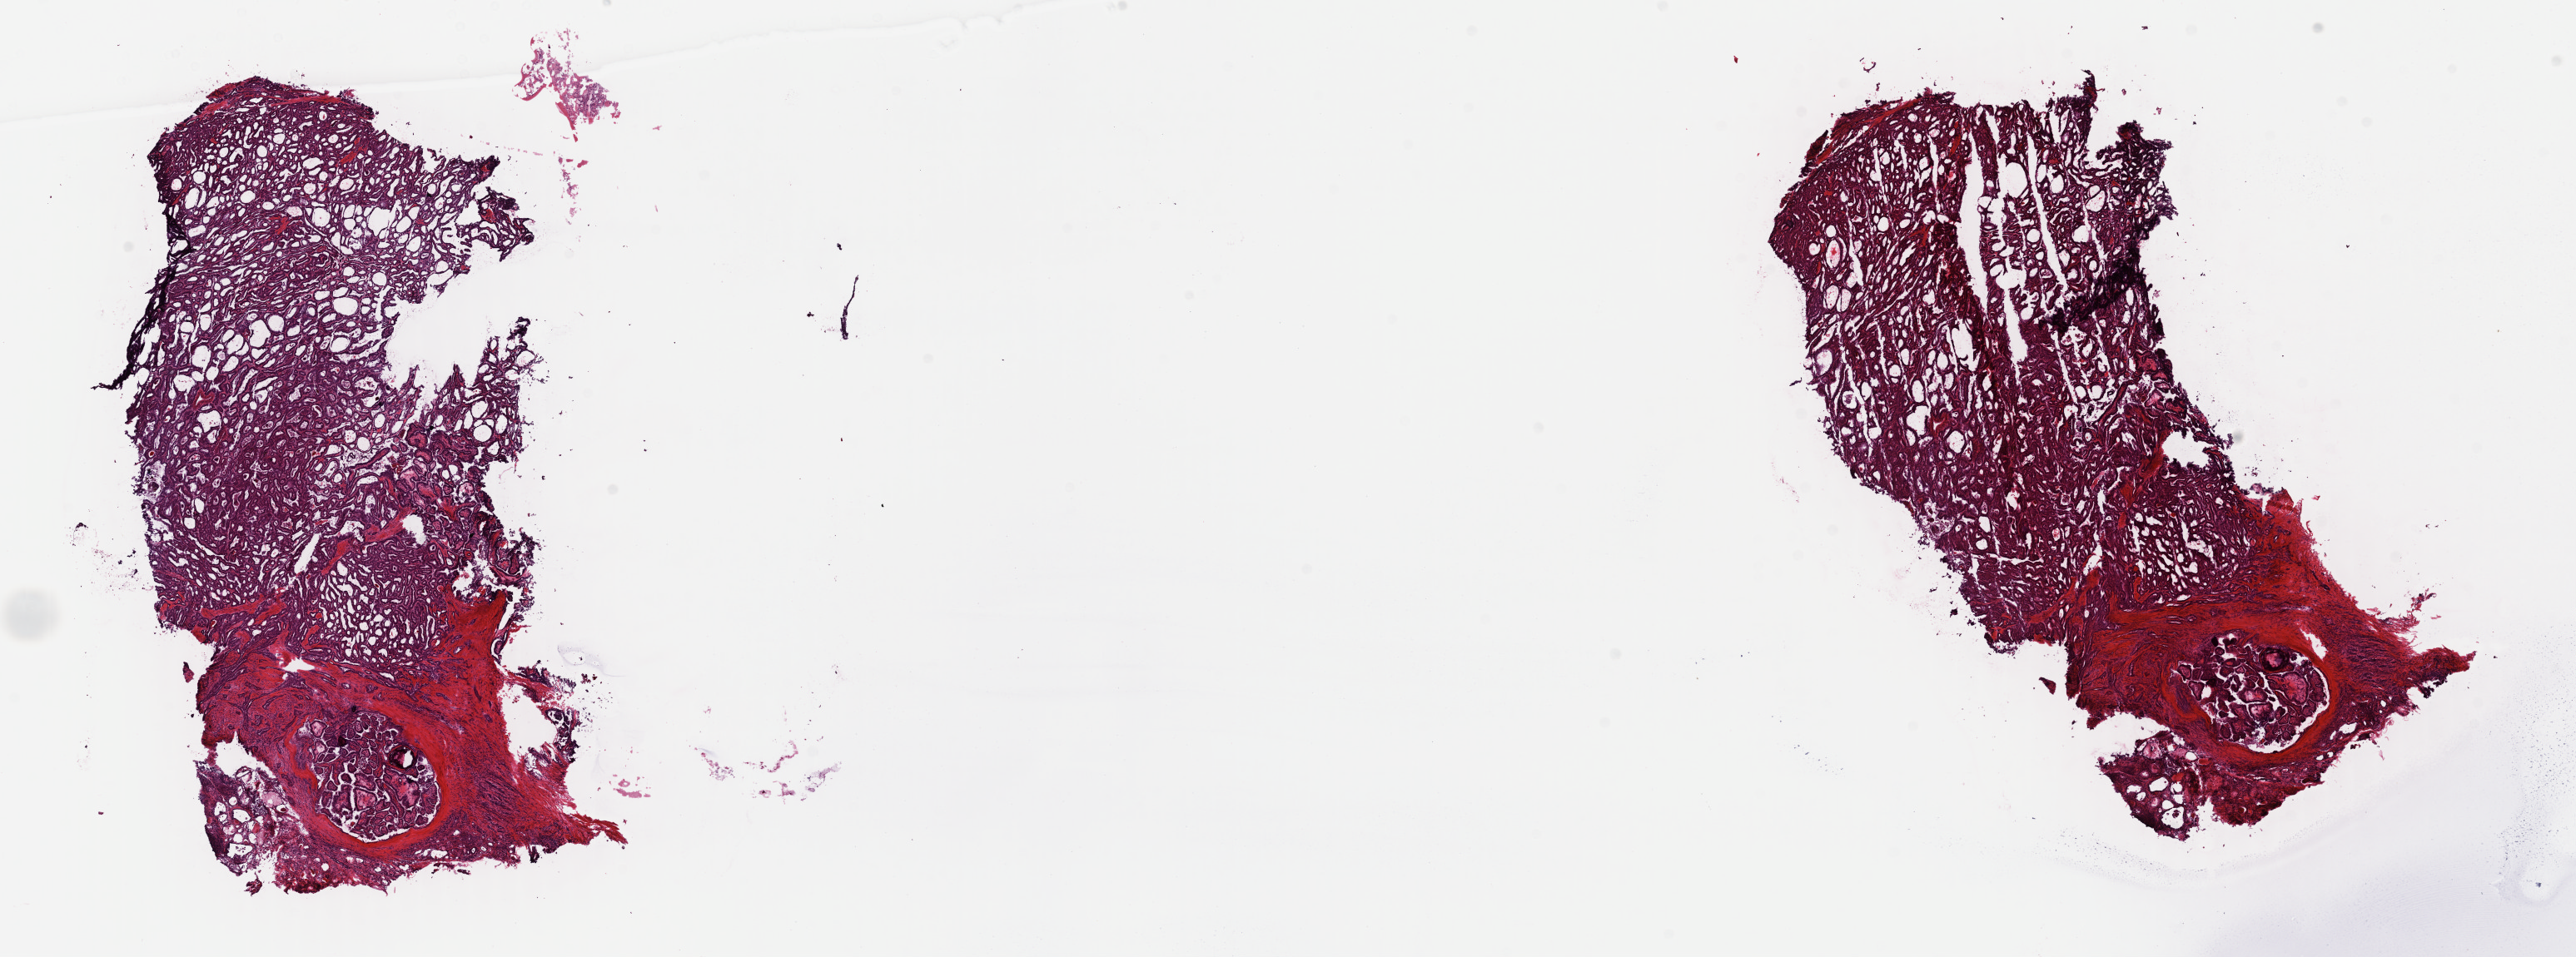
H&E-stained whole-slide image, low-resolution overview of the scanned area, about 24.4 x 9.1 mm. Frozen section from the top of the tissue portion. Primary tumour sample from the thyroid. Patient: male, age at initial diagnosis 43 years. Pathologist review of this section (percent, as recorded): tumour cells 80%, tumour nuclei 80%, normal cells 0%, stromal cells 20%, necrosis 0%. Inflammatory infiltration, as recorded: lymphocyte infiltration 3%, monocyte infiltration 2%, neutrophil infiltration 0%.
- laterality: bilateral
- TNM: T3 N0 M0
- diagnosis: Papillary adenocarcinoma, NOS (thyroid gland)
- AJCC pathologic stage: I (7th edition)